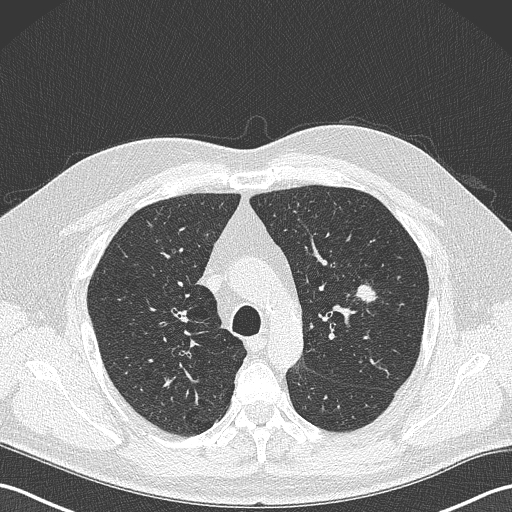
Low-dose screening chest CT, axial slice; baseline annual screen; lung window (W 1500 / L -600 HU); 1 mm slice thickness; slice 100 of 343 in the series. Male, age 61 years at enrolment. Former smoker at enrolment.
Lesion marked by an expert reader, bounding box [x1, y1, x2, y2] px = [340, 275, 385, 317]. The screening reader recorded 2 non-calcified nodules or masses ≥4 mm on this exam (left upper lobe, lingula); which of them this box marks is not recorded. Official screen result: positive, change unspecified: nodule(s) >= 4 mm or enlarging nodule(s), mass(es), or other non-specific abnormalities suspicious for lung cancer. Lung cancer was diagnosed 160 days after this screen: adenocarcinoma, NOS, left upper lobe, poorly differentiated (G3), stage IA (AJCC 6th edition), 28 mm at pathology.